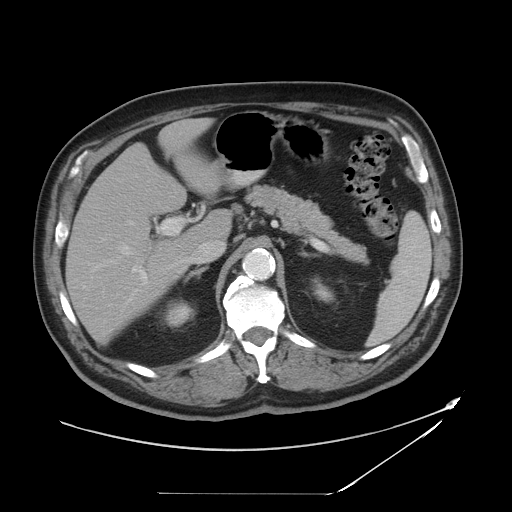
Contrast-enhanced abdominal CT, one axial slice; slice 28 of 49 in the series (ordered by position); intravenous contrast given; soft-tissue window (W 400 / L 40 HU); 5 mm slice thickness; 512 × 512 image matrix, field of view 461 × 461 mm. Male patient, age 72 years. Case-level facts recorded for this patient, not image findings: diagnosis: colorectal cancer liver metastases, imaged before liver resection.
Outlined on this slice (expert manual segmentation):
- hepatic veins: bounding box [x1, y1, x2, y2] px = [90, 181, 149, 272]
- liver: [66, 120, 228, 339]
- planned liver remnant (the part of the liver to remain after resection): [66, 167, 190, 339]
- portal vein (with intrahepatic branches): [131, 218, 191, 284]